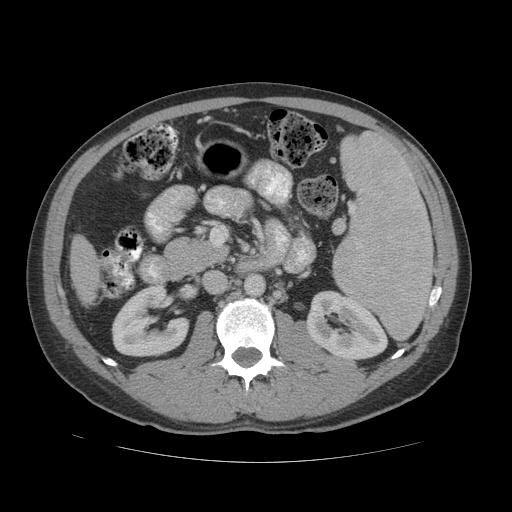
Contrast-enhanced abdominal CT (liver protocol), one axial slice; slice 12 of 81 in the series (ordered by position); 140 kVp; soft-tissue window (W 400 / L 40 HU); 2.5 mm slice thickness; 512 × 512 image matrix, field of view 400 × 400 mm. From the clinical record (not read from this slice): diagnosis: hepatocellular carcinoma (patient treated with transarterial chemoembolisation; whether this scan precedes or follows treatment is not stated here); TNM stage (as recorded): Stage-IVB; Child-Pugh class: B; tumour differentiation: well differentiated; tumour nodularity: multinodular.
Structures marked on this image (semi-automatic segmentation, software-assisted and operator-edited):
- liver parenchyma outside the tumour (the mass and vessels are separate outlines, so this box may not span the whole liver): bounding box [x1, y1, x2, y2] px = [70, 236, 100, 302]